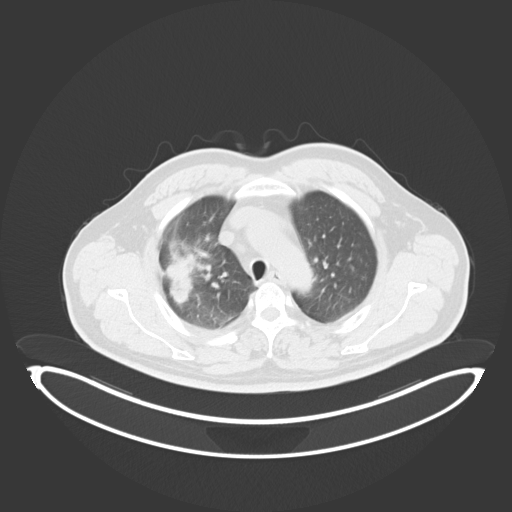
Chest CT, one axial slice. Slice 226 of 284 in the series (ordered by position). Reconstruction kernel B30f. Lung window (W 1500 / L -600 HU). 3 mm slice thickness. 512 × 512 image matrix, field of view 500 × 500 mm. Male patient, age 55 years. From the clinical record (not read from this slice): clinical TNM (as recorded): T3 N2 M1.
Outlined on this slice (bounding box drawn by a radiologist):
- lung tumour (recorded histology: adenocarcinoma): bounding box (x1, y1, x2, y2) in pixels: (161, 241, 200, 306)